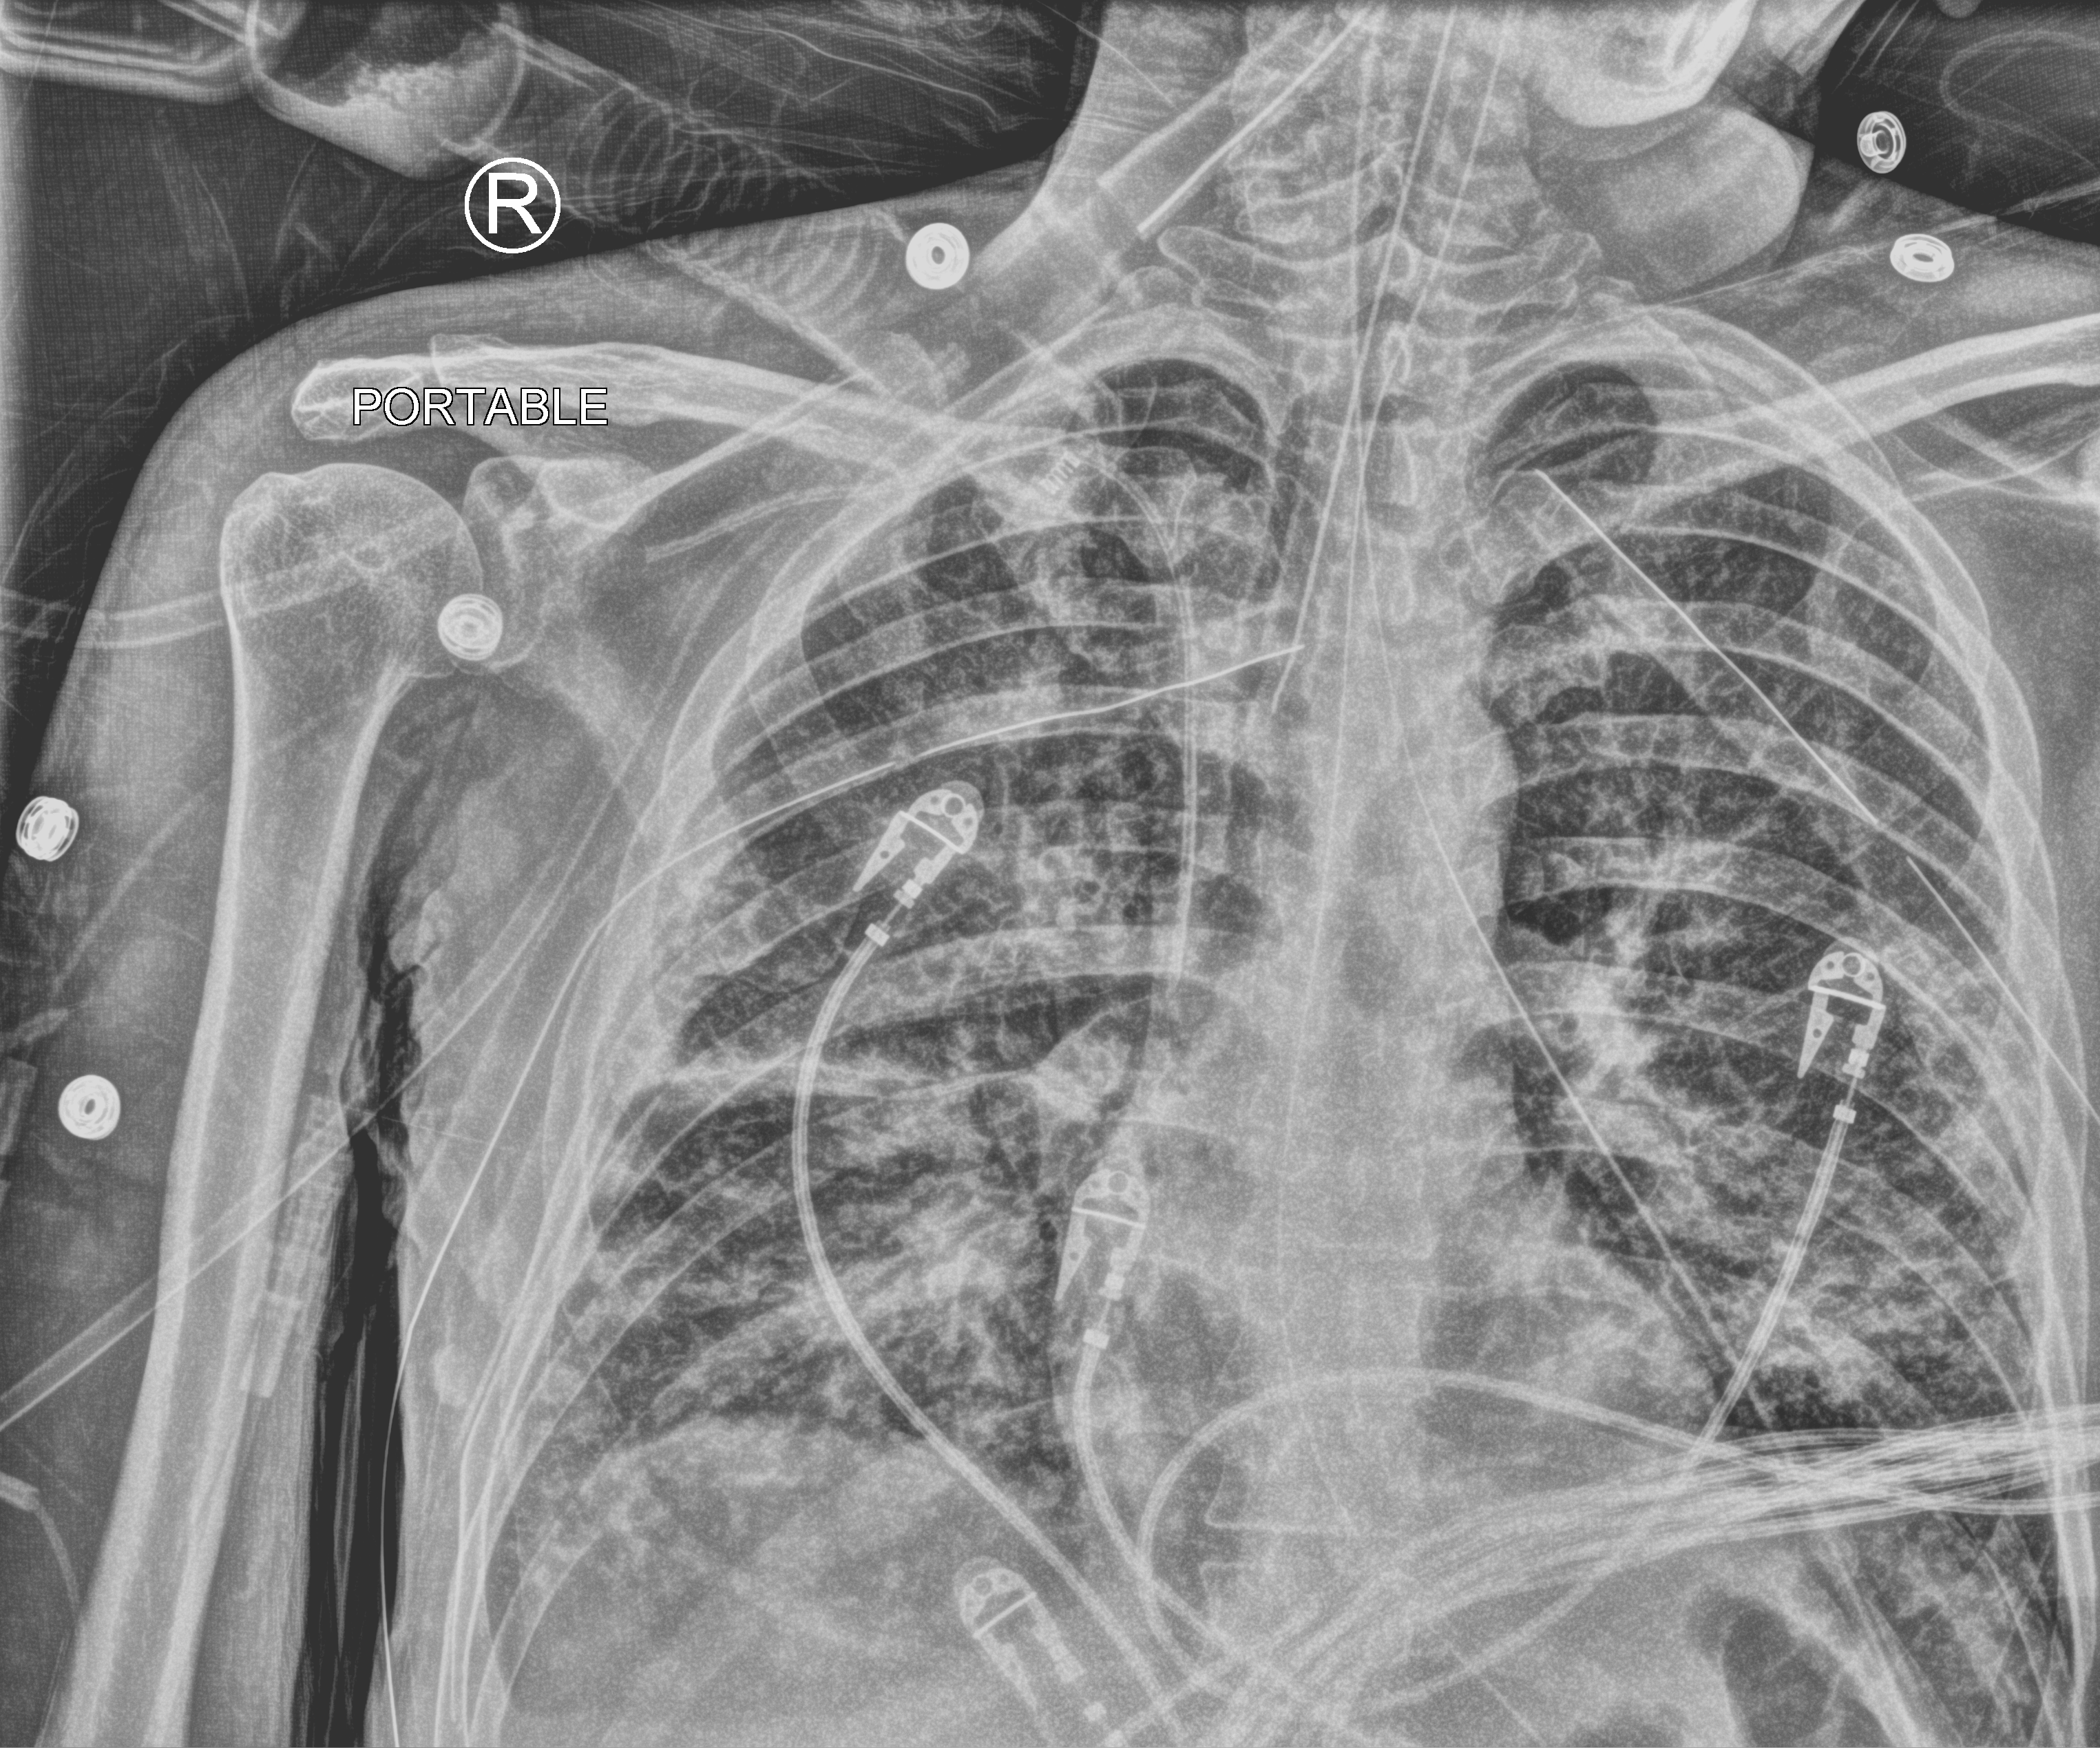
Chest X-ray (portable); anteroposterior (AP) projection. Male patient hospitalised with COVID-19, age 18–59 years.
Admission-level facts for this patient (not findings on this image; timing relative to this image not recorded):
- mechanically ventilated during this hospital stay: yes